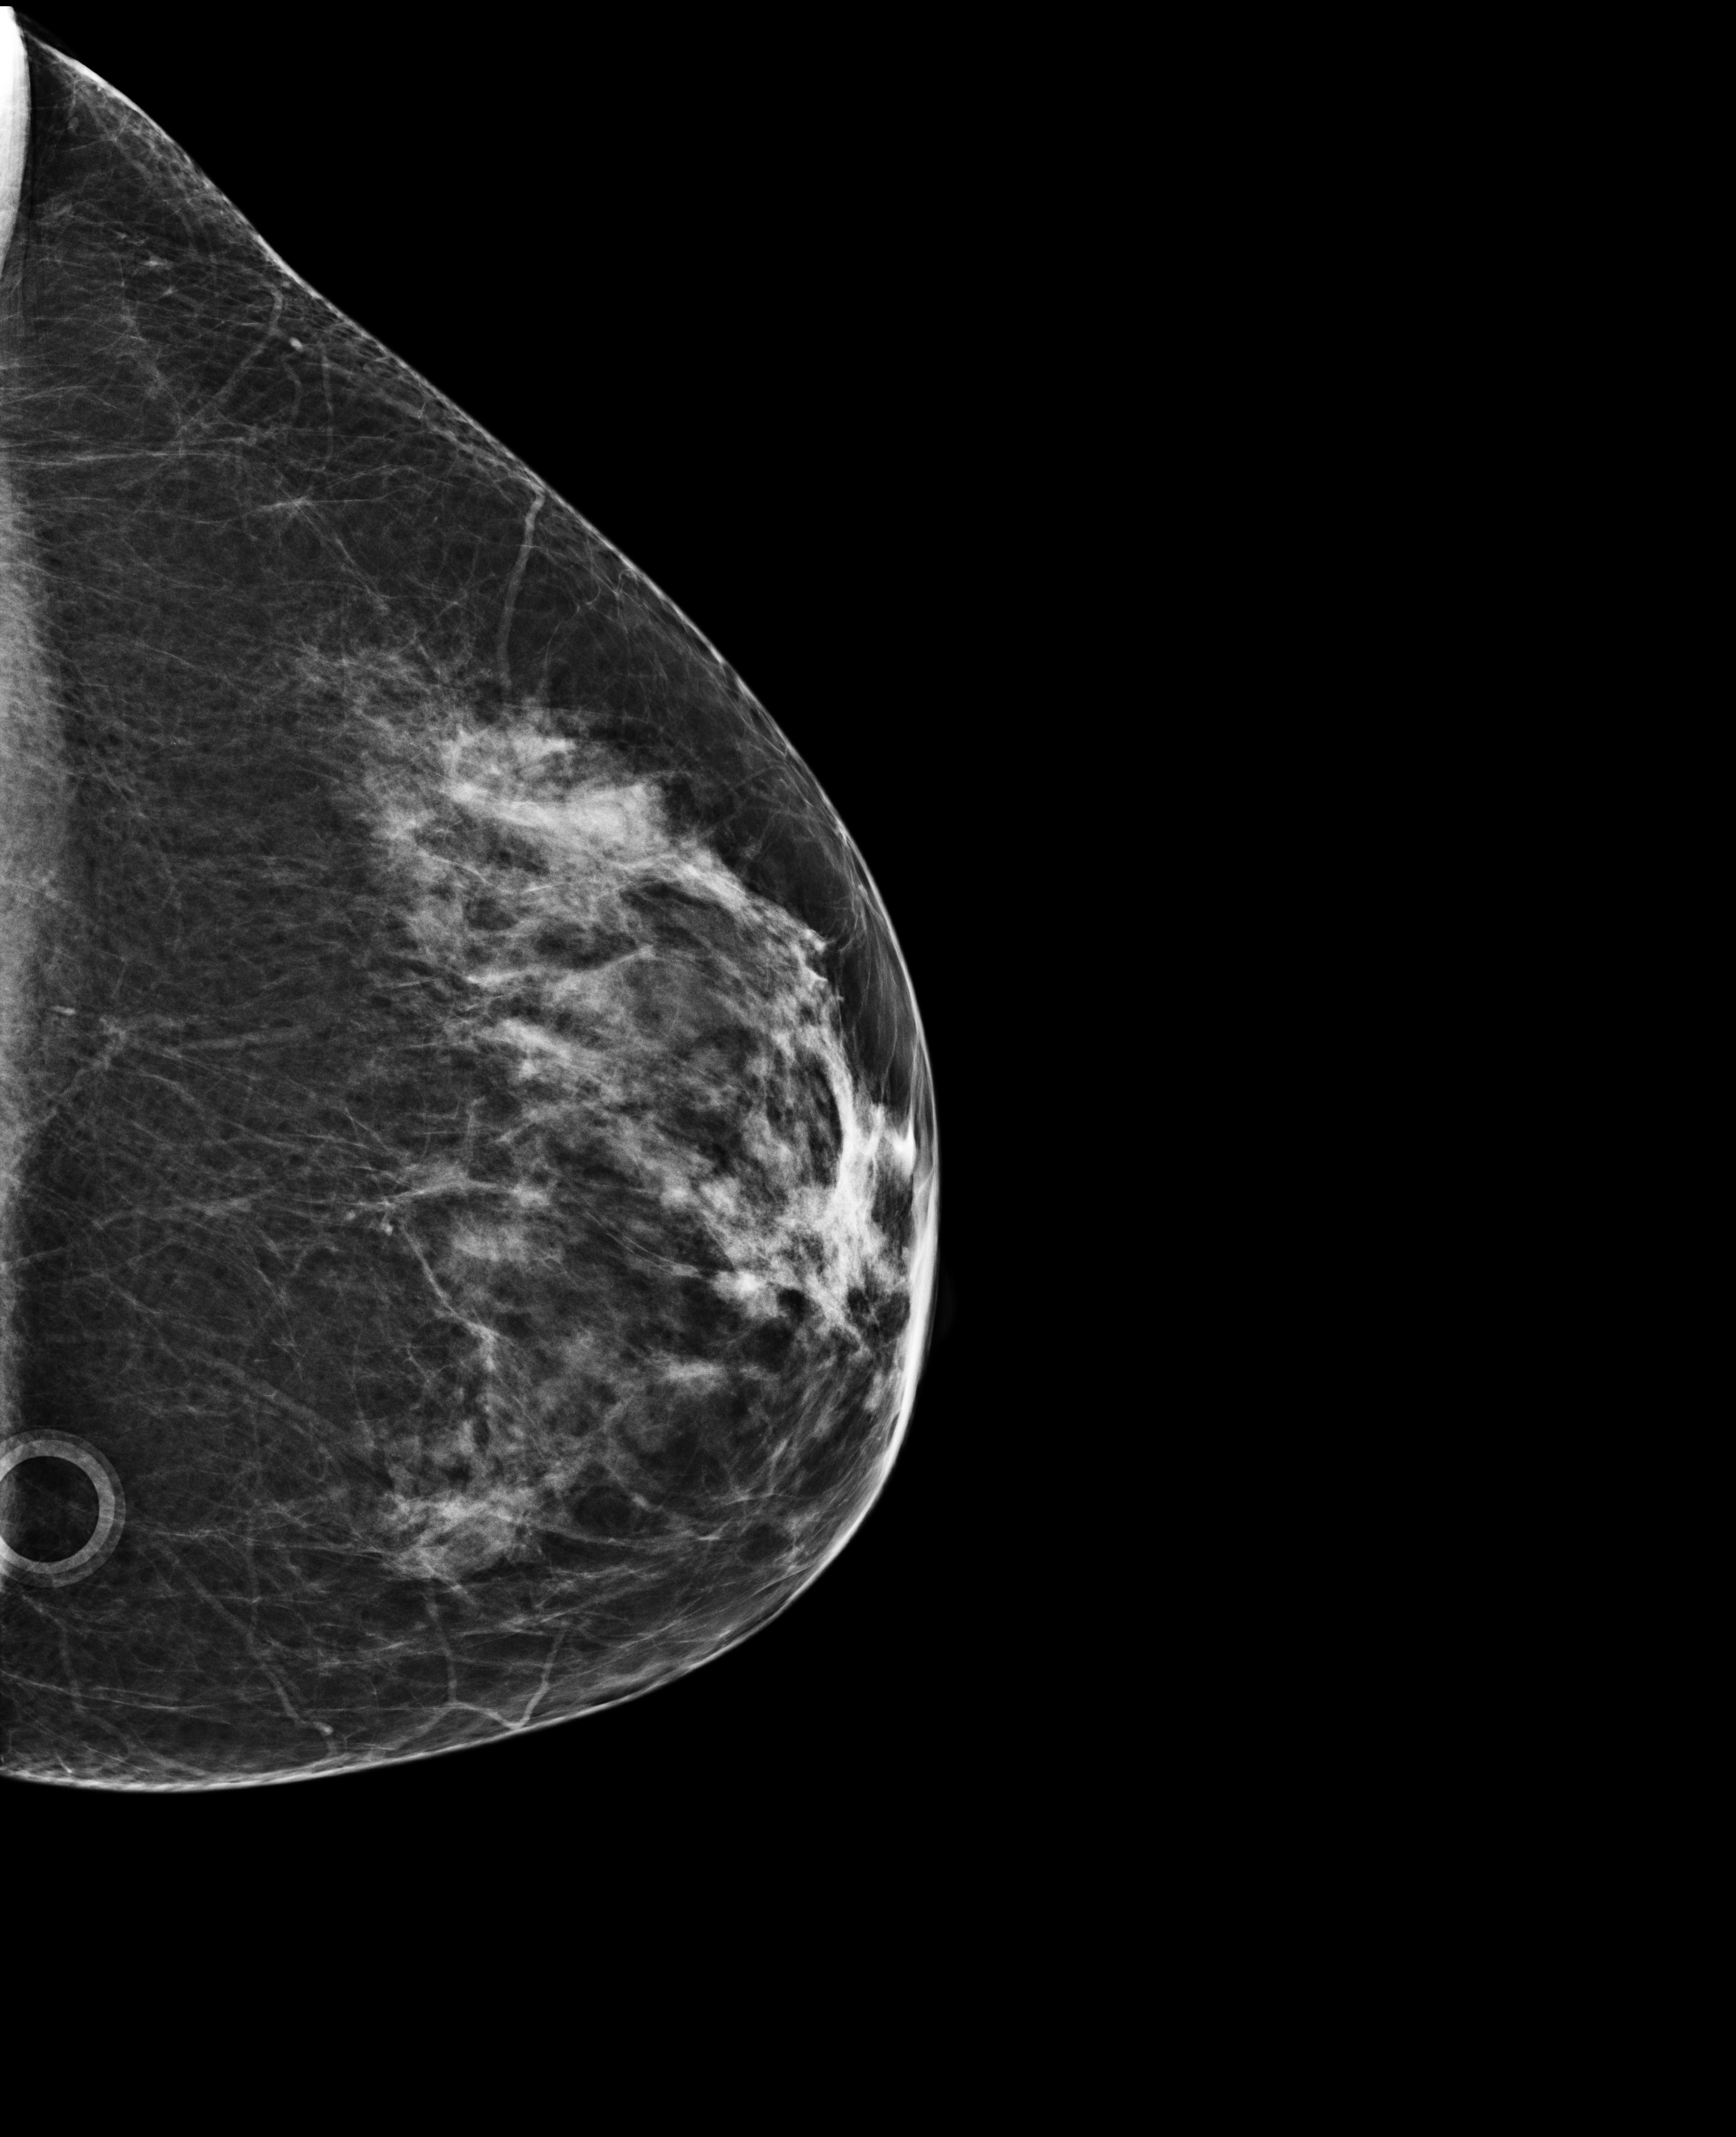
Full-field digital mammogram (FFDM), left breast, laterally exaggerated craniocaudal (XCCL) view, screening examination, compressed breast thickness 54 mm, system: Selenia Dimensions. Female patient, age 63 years.
Breast density at the screening exam (both breasts): heterogeneously dense (BI-RADS density category c). Final BI-RADS category for the screening round (tomosynthesis exam, both breasts): category 1. Recall: no recall after this screen.